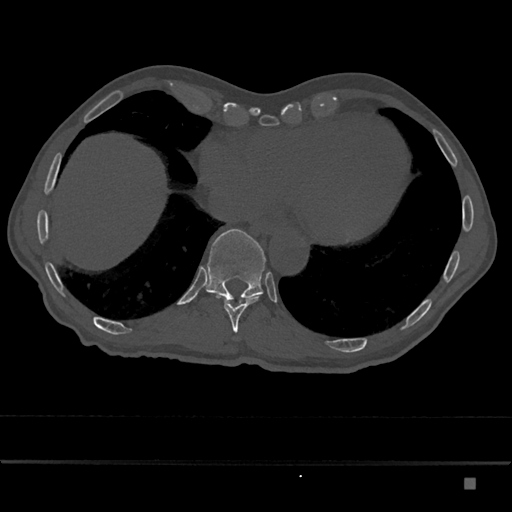
CT including the spine, one axial slice; reconstruction kernel Br40s/3; bone window (W 1800 / L 400 HU); 512 × 512 image matrix, field of view 390 × 390 mm. Male patient, age 72 years. From the clinical record (not read from this slice): primary cancer: prostate.
Annotated regions visible in this slice (semi-automatically segmented with operator editing):
- T10 vertebra: bounding box <217,296,259,333> (left, top, right, bottom; pixels)
- T11 vertebra: <205,229,266,301>